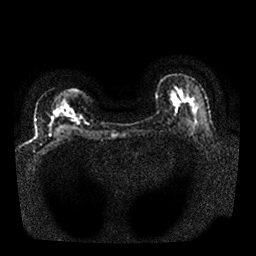
Breast MRI, one axial slice; slice 14 of 25 in the series (ordered by position); diffusion-weighted series; image 2 of 4 stored at this slice position (different b-values; order by instance number); 1.5 T; 256 × 256 image matrix, field of view 340 × 340 mm. Female patient.
Annotated regions visible in this slice (outlined manually by an expert reader):
- tumour on diffusion-weighted imaging: bounding box (x1, y1, x2, y2) in pixels: (70, 113, 82, 123)